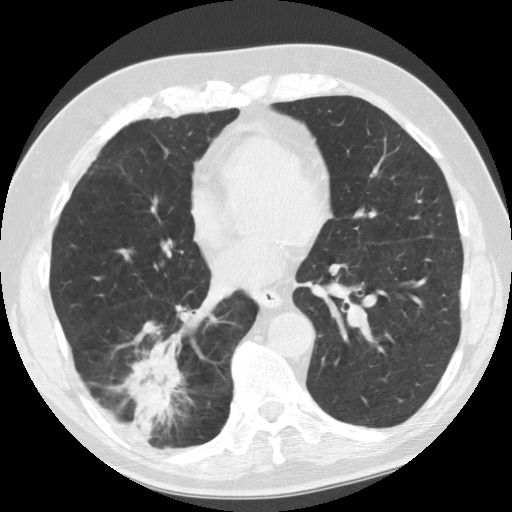
Axial slice from a low-dose chest CT screening exam; baseline annual screen; lung window (W 1500 / L -600 HU); 2.5 mm slice thickness; standard (soft-tissue) reconstruction kernel (STANDARD); 120 kVp; 512 × 512 image matrix. Male, age 69 years at enrolment.
Expert reader's lesion annotation, bounding box <111,332,197,441> (left, top, right, bottom; pixels). The screening reader recorded 2 non-calcified nodules or masses ≥4 mm on this exam (right lower lobe, right lower lobe); which of them this box marks is not recorded. Participant outcome: lung cancer diagnosed 40 days after this screen — adenocarcinoma, NOS, right lower lobe, stage IIB (AJCC 6th edition), 45 mm at pathology.